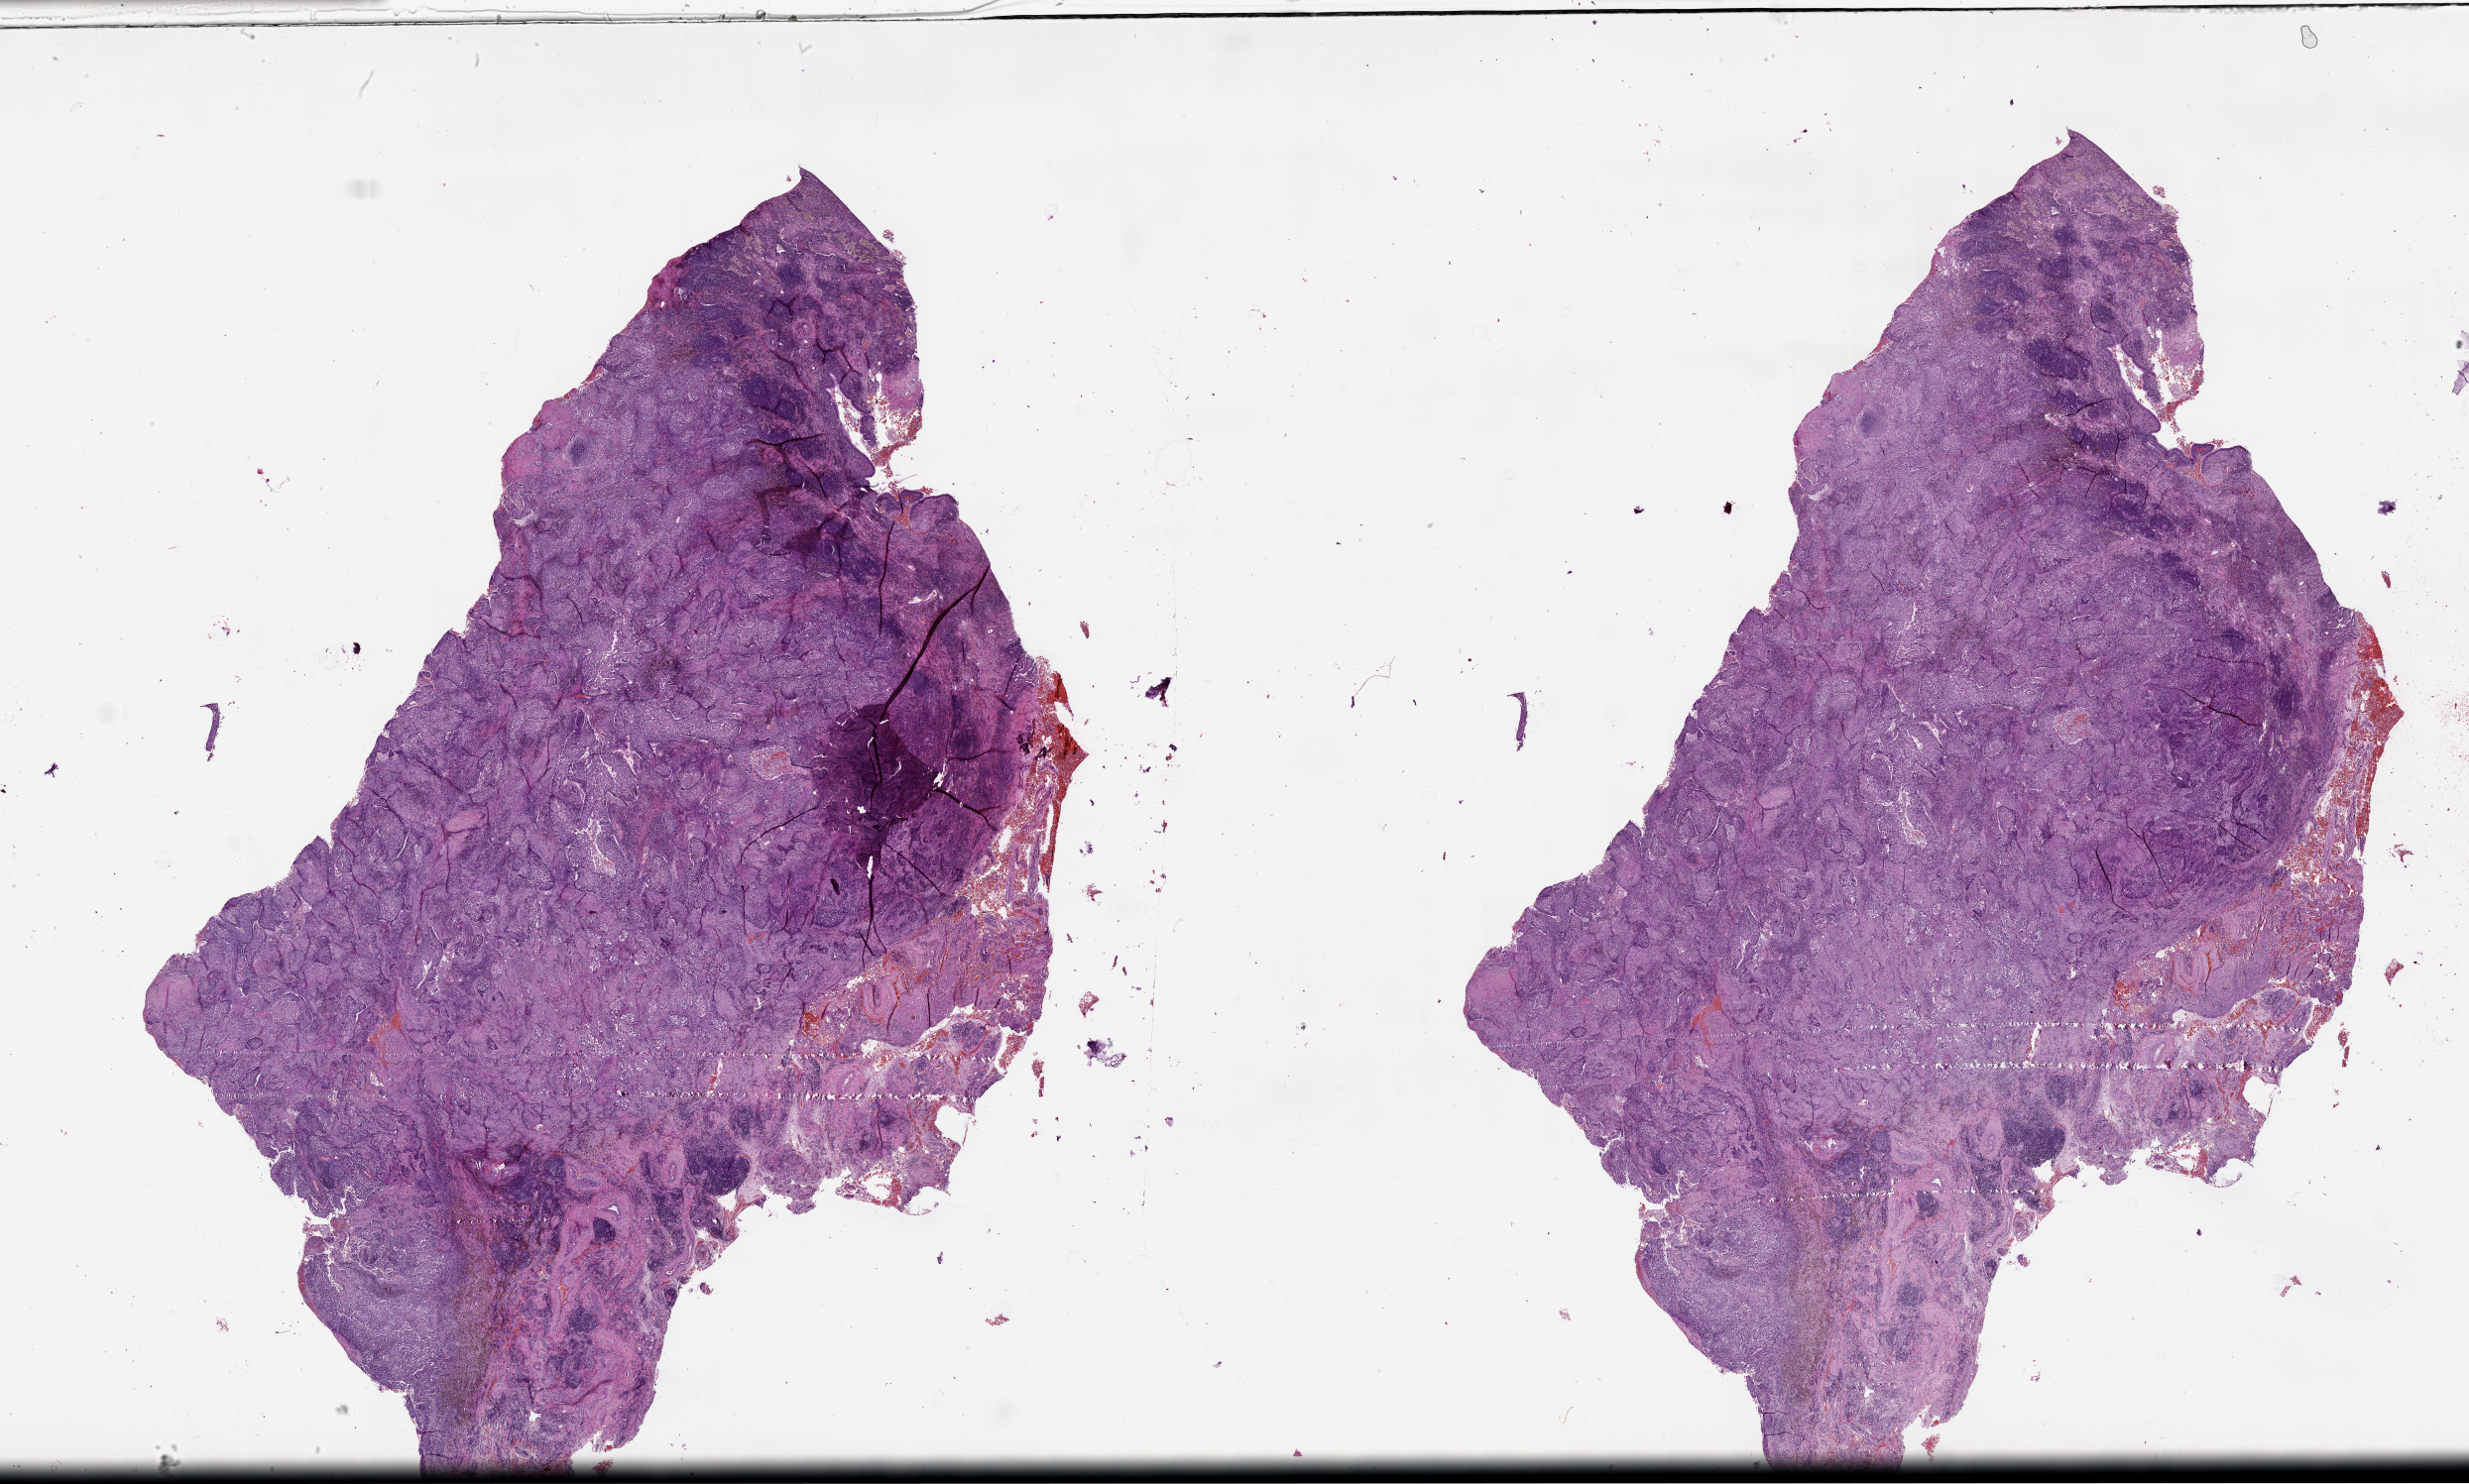
Hematoxylin and eosin (H&E) stained whole-slide image — shown as a low-resolution overview of the whole scanned area (about 40.1 x 24.1 mm, acquisition: 20x scan), tumour tissue sample, lung. Patient: male, age 49 years.
Patient diagnosis (cohort enrolment): squamous cell carcinoma (lung).